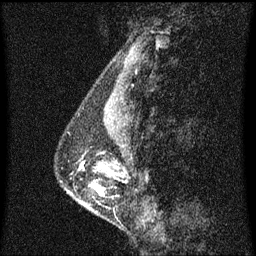
Breast MRI (dynamic contrast-enhanced), one sagittal slice; position 21 of 60 along the scan axis; dynamic contrast-enhanced series, image 2 of 3 at this slice position (ordered by acquisition); 1.5 T; TE 4.2 ms, TR 8.4 ms; 256 × 256 image matrix, field of view 200 × 200 mm. Patient: female, 40 years. Case-level facts recorded for this patient, not image findings: setting: breast cancer imaged before/during neoadjuvant chemotherapy; receptor status: triple-negative.
Structures marked on this image (semi-automatic segmentation, software-assisted and operator-edited):
- analysis volume of interest (the breast-tissue region the enhancement analysis was run in; not a lesion): bounding box <68,128,120,211> (left, top, right, bottom; pixels)
- tumour enhancement mask (voxels above the 70 % enhancement threshold inside the analysis volume of interest): <98,190,100,193>